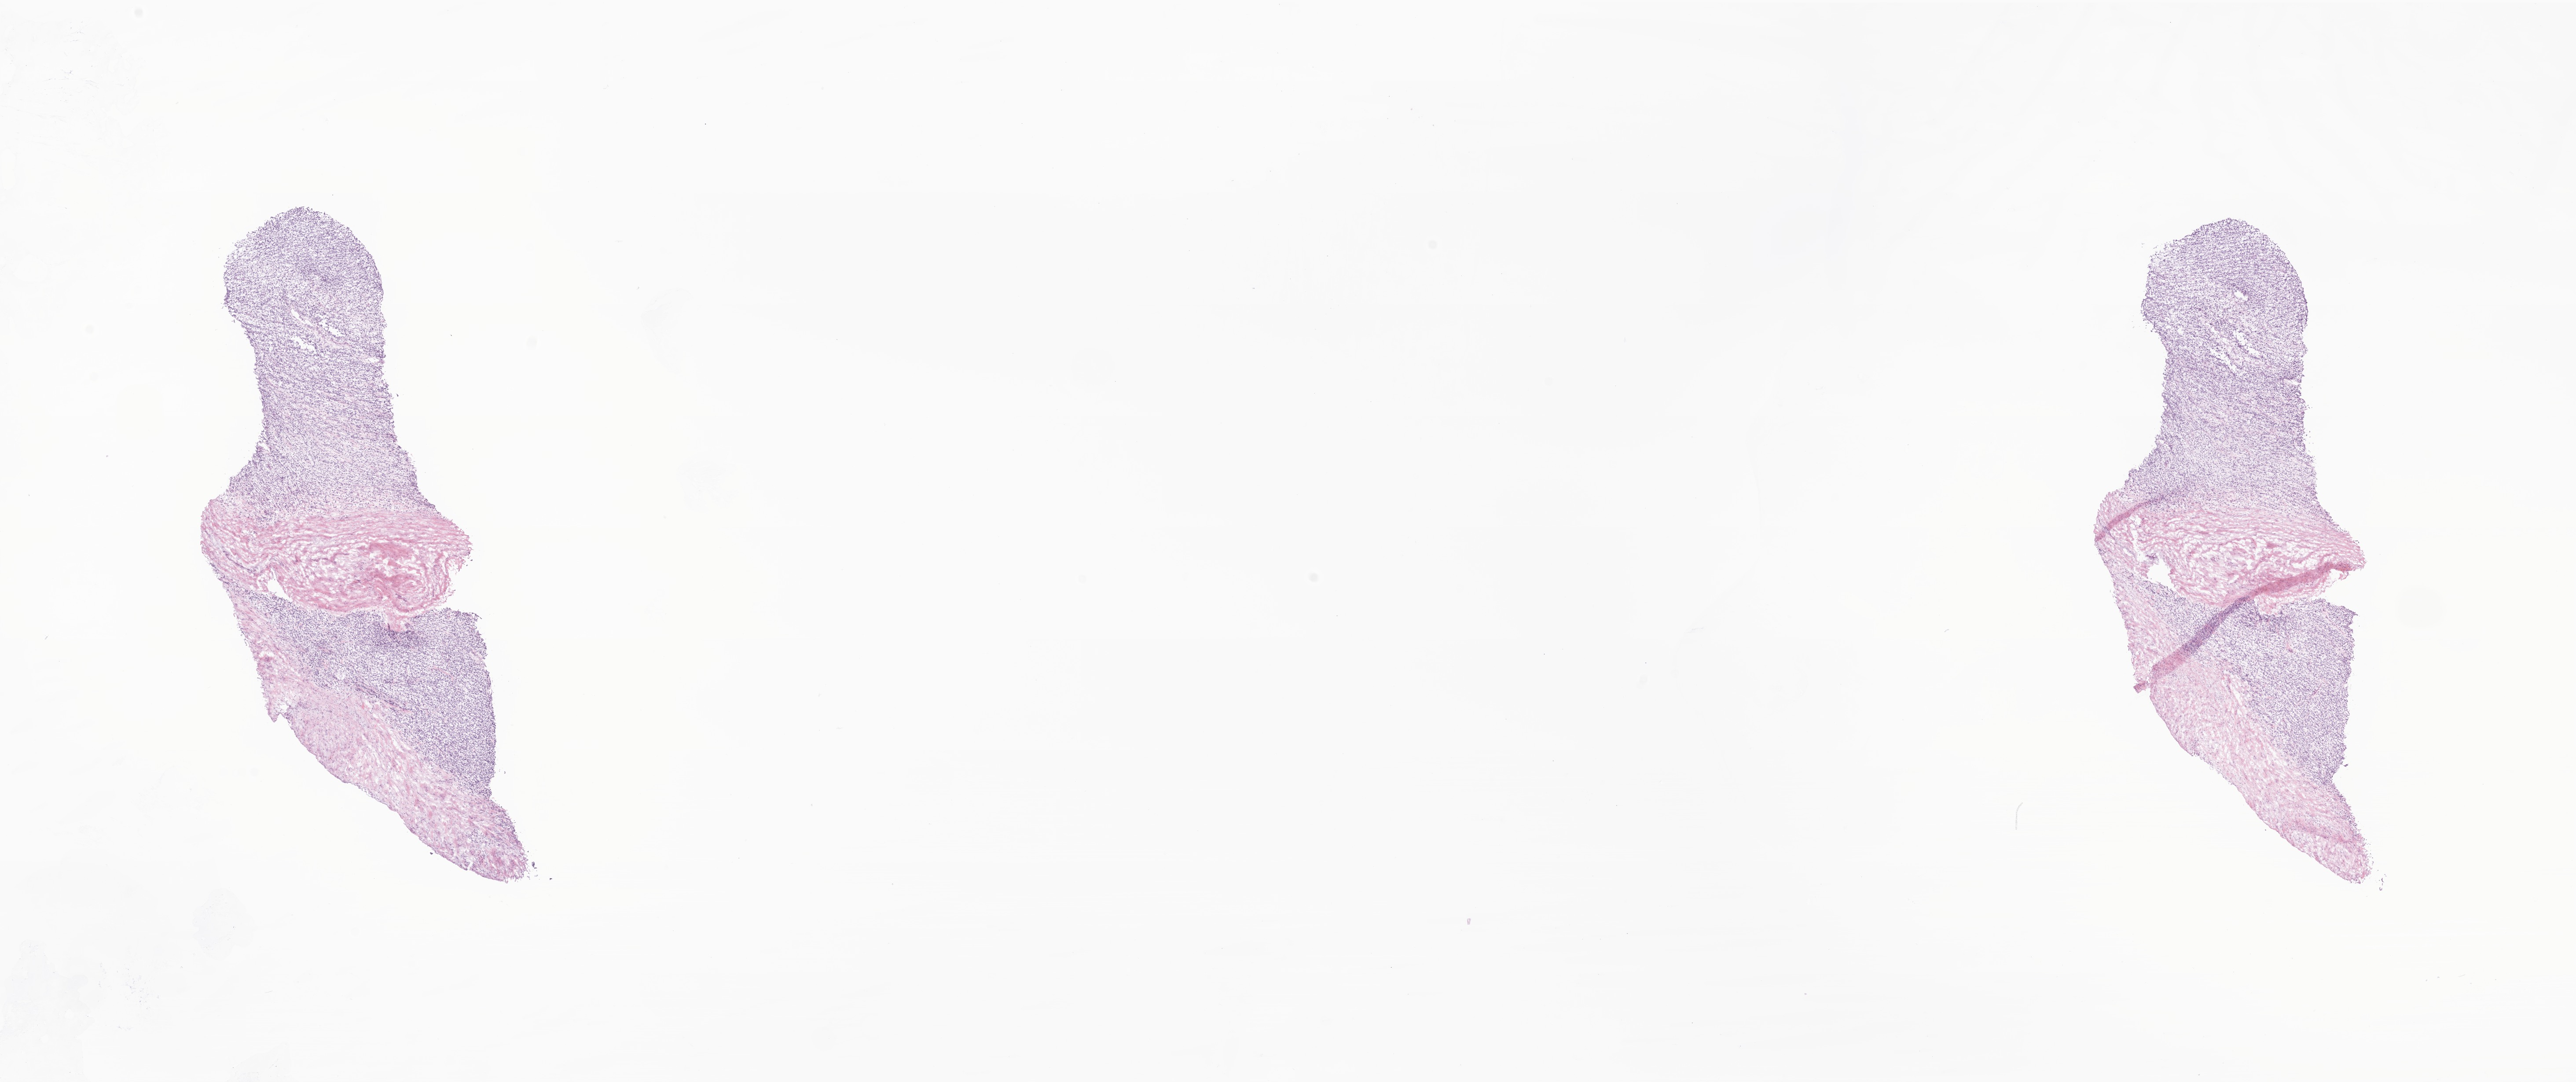
Whole-slide image, H&E stain of tumor tissue from the testis — shown as a low-resolution overview of the whole scanned area (about 24.7 x 10.4 mm); cryosection (OCT / tissue freezing medium). Patient: male, age 202 months (16 years 10 months).
• diagnosis (ICD-O-3 morphology term): Rhabdomyosarcoma, NOS